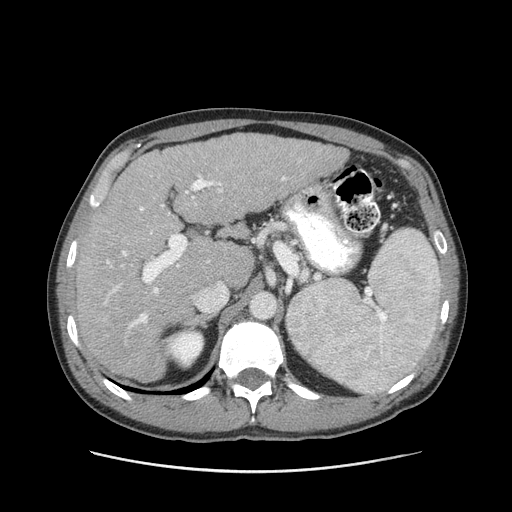
Contrast-enhanced abdominal CT (liver protocol), one axial slice. Position 60 of 93 along the scan axis. Reconstruction kernel STANDARD. Soft-tissue window (W 400 / L 40 HU). 2.5 mm slice thickness. 512 × 512 image matrix, field of view 380 × 380 mm. From the clinical record (not read from this slice): diagnosis: hepatocellular carcinoma (patient treated with transarterial chemoembolisation; whether this scan precedes or follows treatment is not stated here); TNM stage (as recorded): Stage-II.
Structures marked on this image (semi-automatic segmentation, software-assisted and operator-edited):
- liver parenchyma outside the tumour (the mass and vessels are separate outlines, so this box may not span the whole liver): bounding box [x1, y1, x2, y2] px = [76, 134, 348, 382]
- liver vessels: [104, 175, 286, 329]